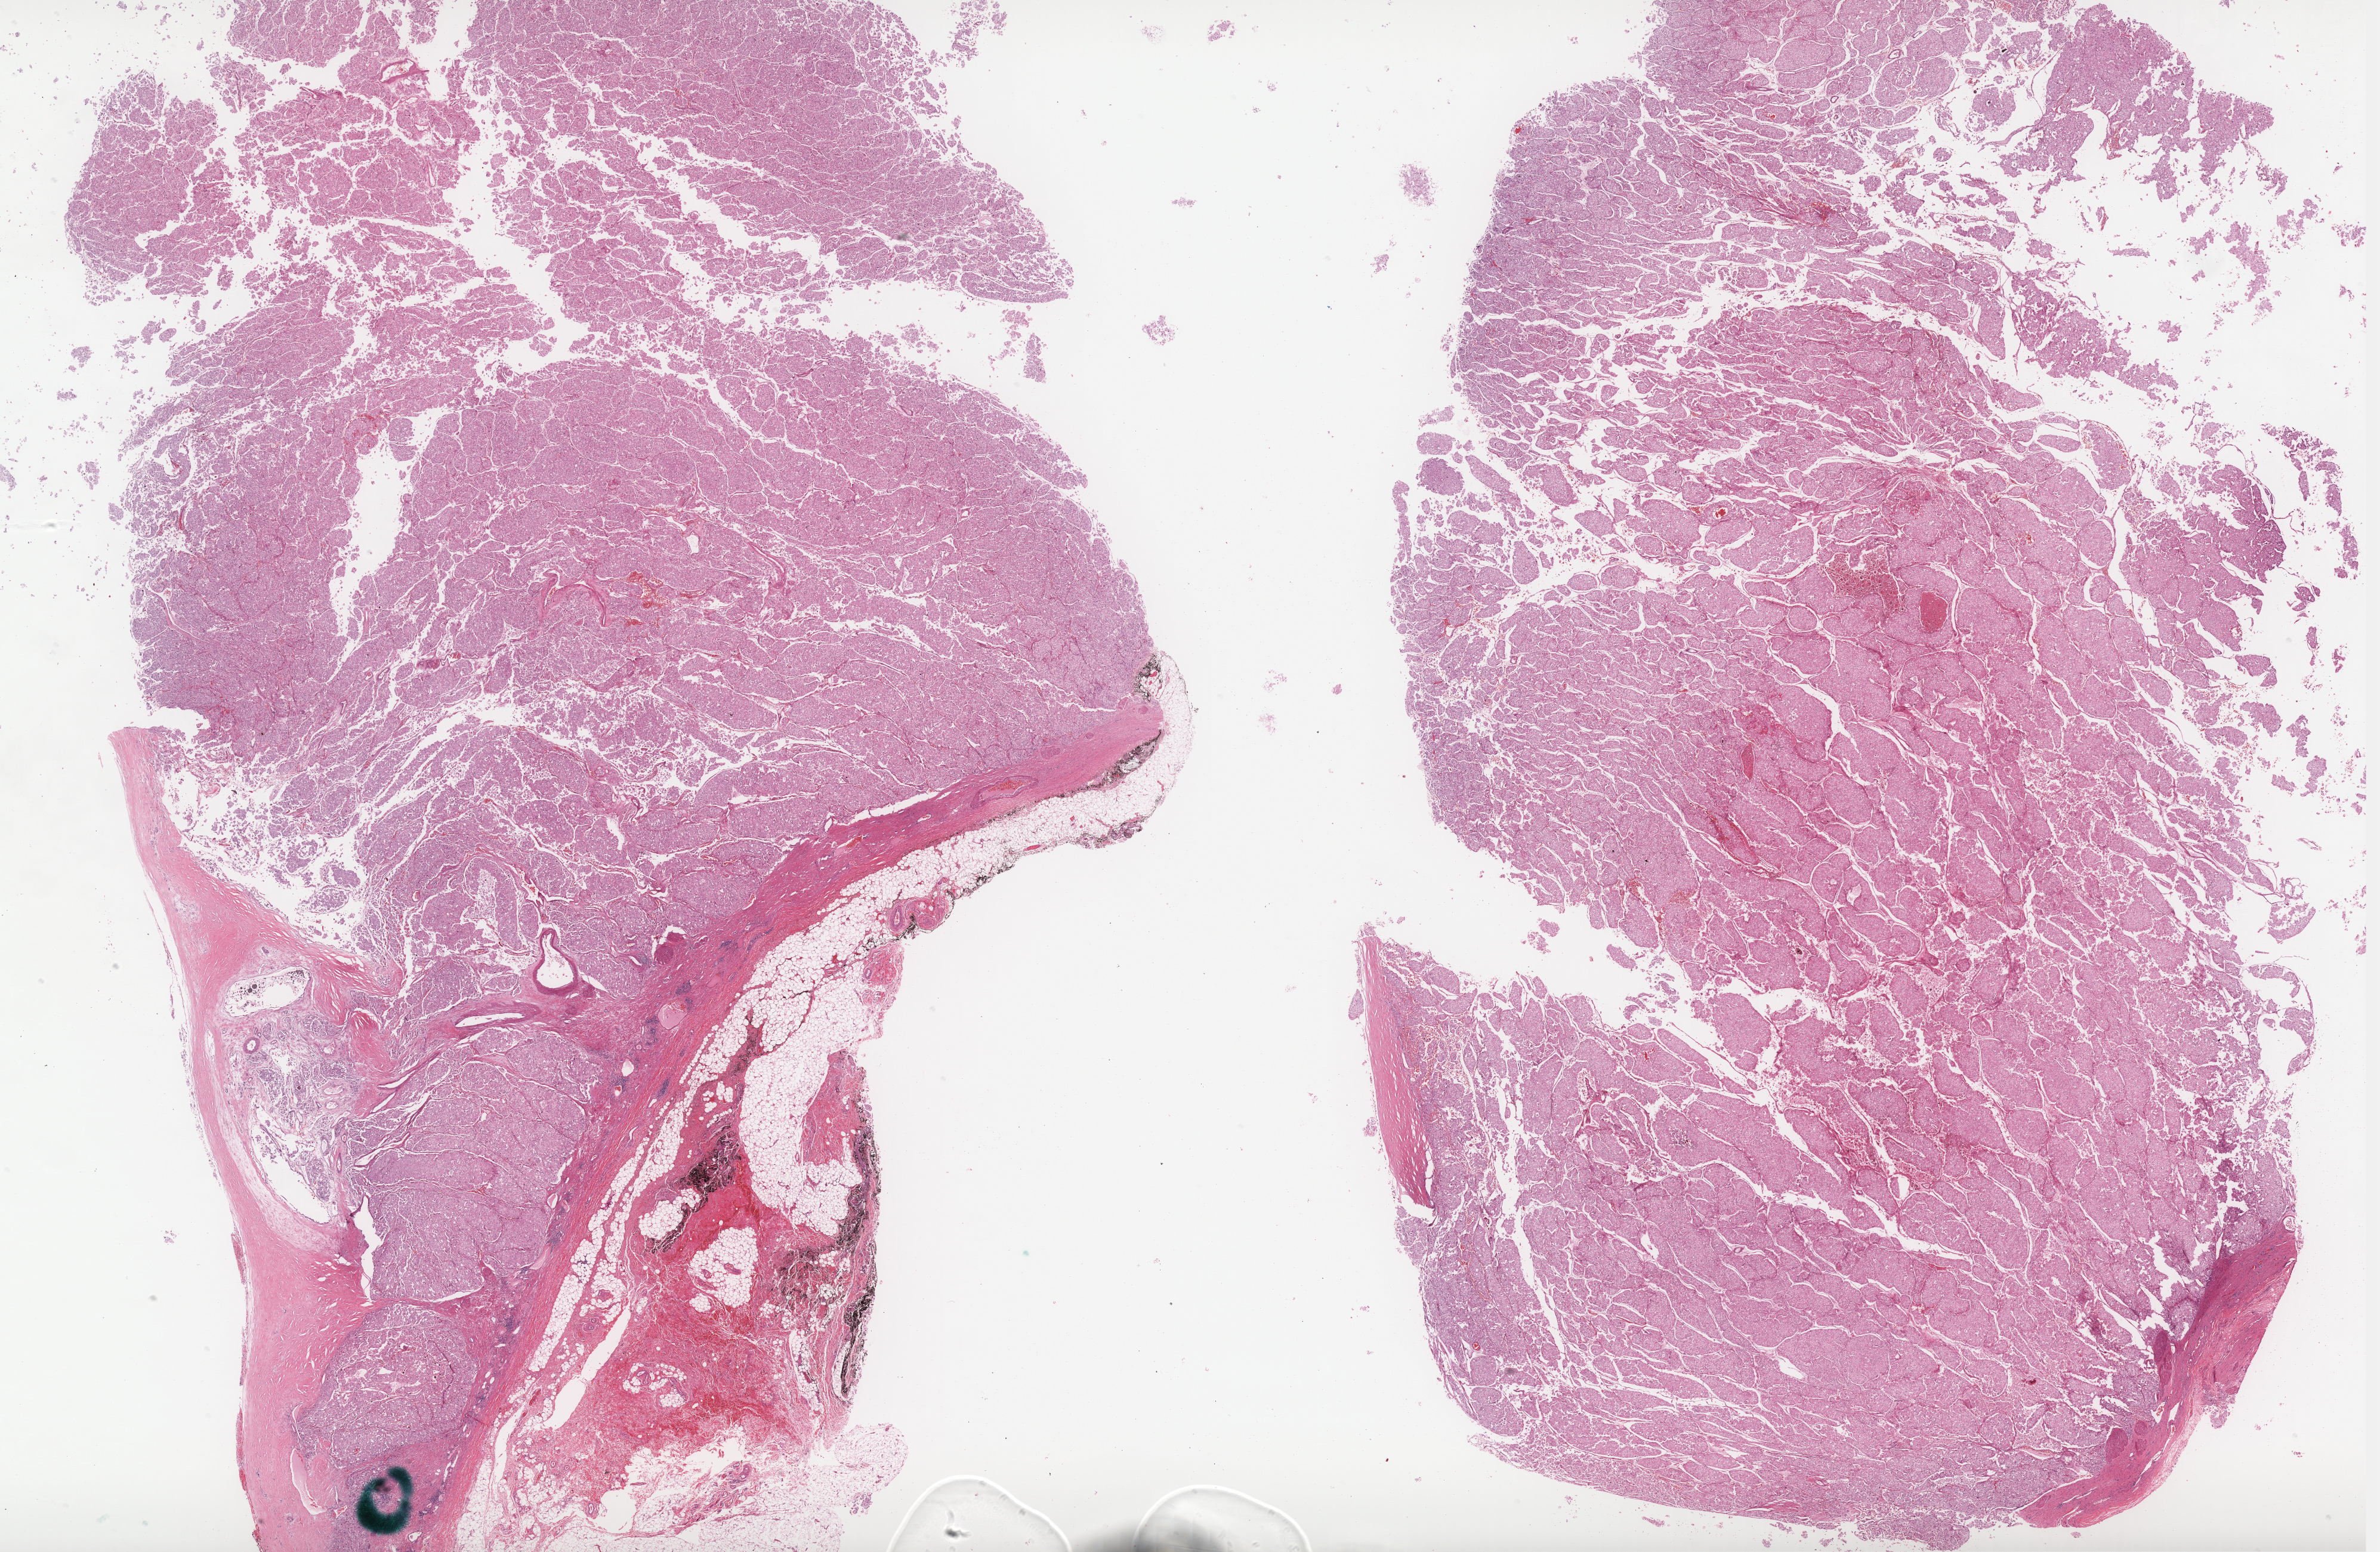
Hematoxylin and eosin (H&E) stained whole-slide image, low-resolution overview of the scanned area, about 31.9 x 20.8 mm (acquisition: 40x scan); FFPE section; kidney, primary tumour sample. Patient: male, age at initial diagnosis 55 years.
Laterality: right. Histologic diagnosis: Renal cell carcinoma, chromophobe type. Lymph nodes positive (case pathology): 0 of 1 examined. AJCC pathologic stage: I (6th edition).